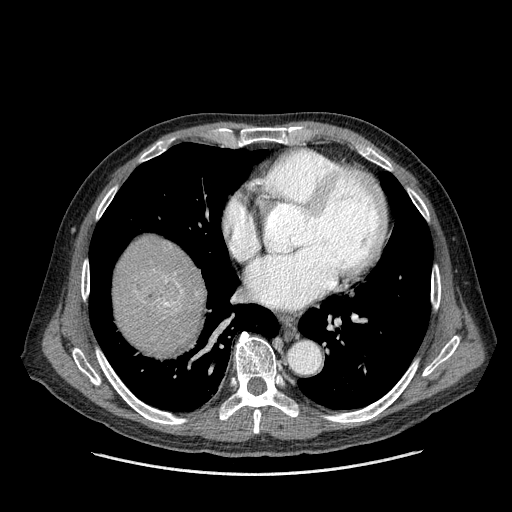
Contrast-enhanced abdominal CT (liver protocol), one axial slice; slice 156 of 180 in the series (ordered by position); reconstruction kernel STANDARD; 120 kVp; one of 2 acquisitions stored at this slice position; soft-tissue window (W 400 / L 40 HU); 2.5 mm slice thickness; 512 × 512 image matrix, field of view 420 × 420 mm. Case-level facts recorded for this patient, not image findings: diagnosis: hepatocellular carcinoma (patient treated with transarterial chemoembolisation; whether this scan precedes or follows treatment is not stated here); TNM stage (as recorded): Stage-II; Child-Pugh class: A; tumour differentiation: well differentiated; tumour nodularity: multinodular.
Annotated regions visible in this slice (semi-automatic segmentation, software-assisted and operator-edited):
- liver parenchyma outside the tumour (the mass and vessels are separate outlines, so this box may not span the whole liver): bounding box <114,234,206,355> (left, top, right, bottom; pixels)
- mass: <133,266,183,311>